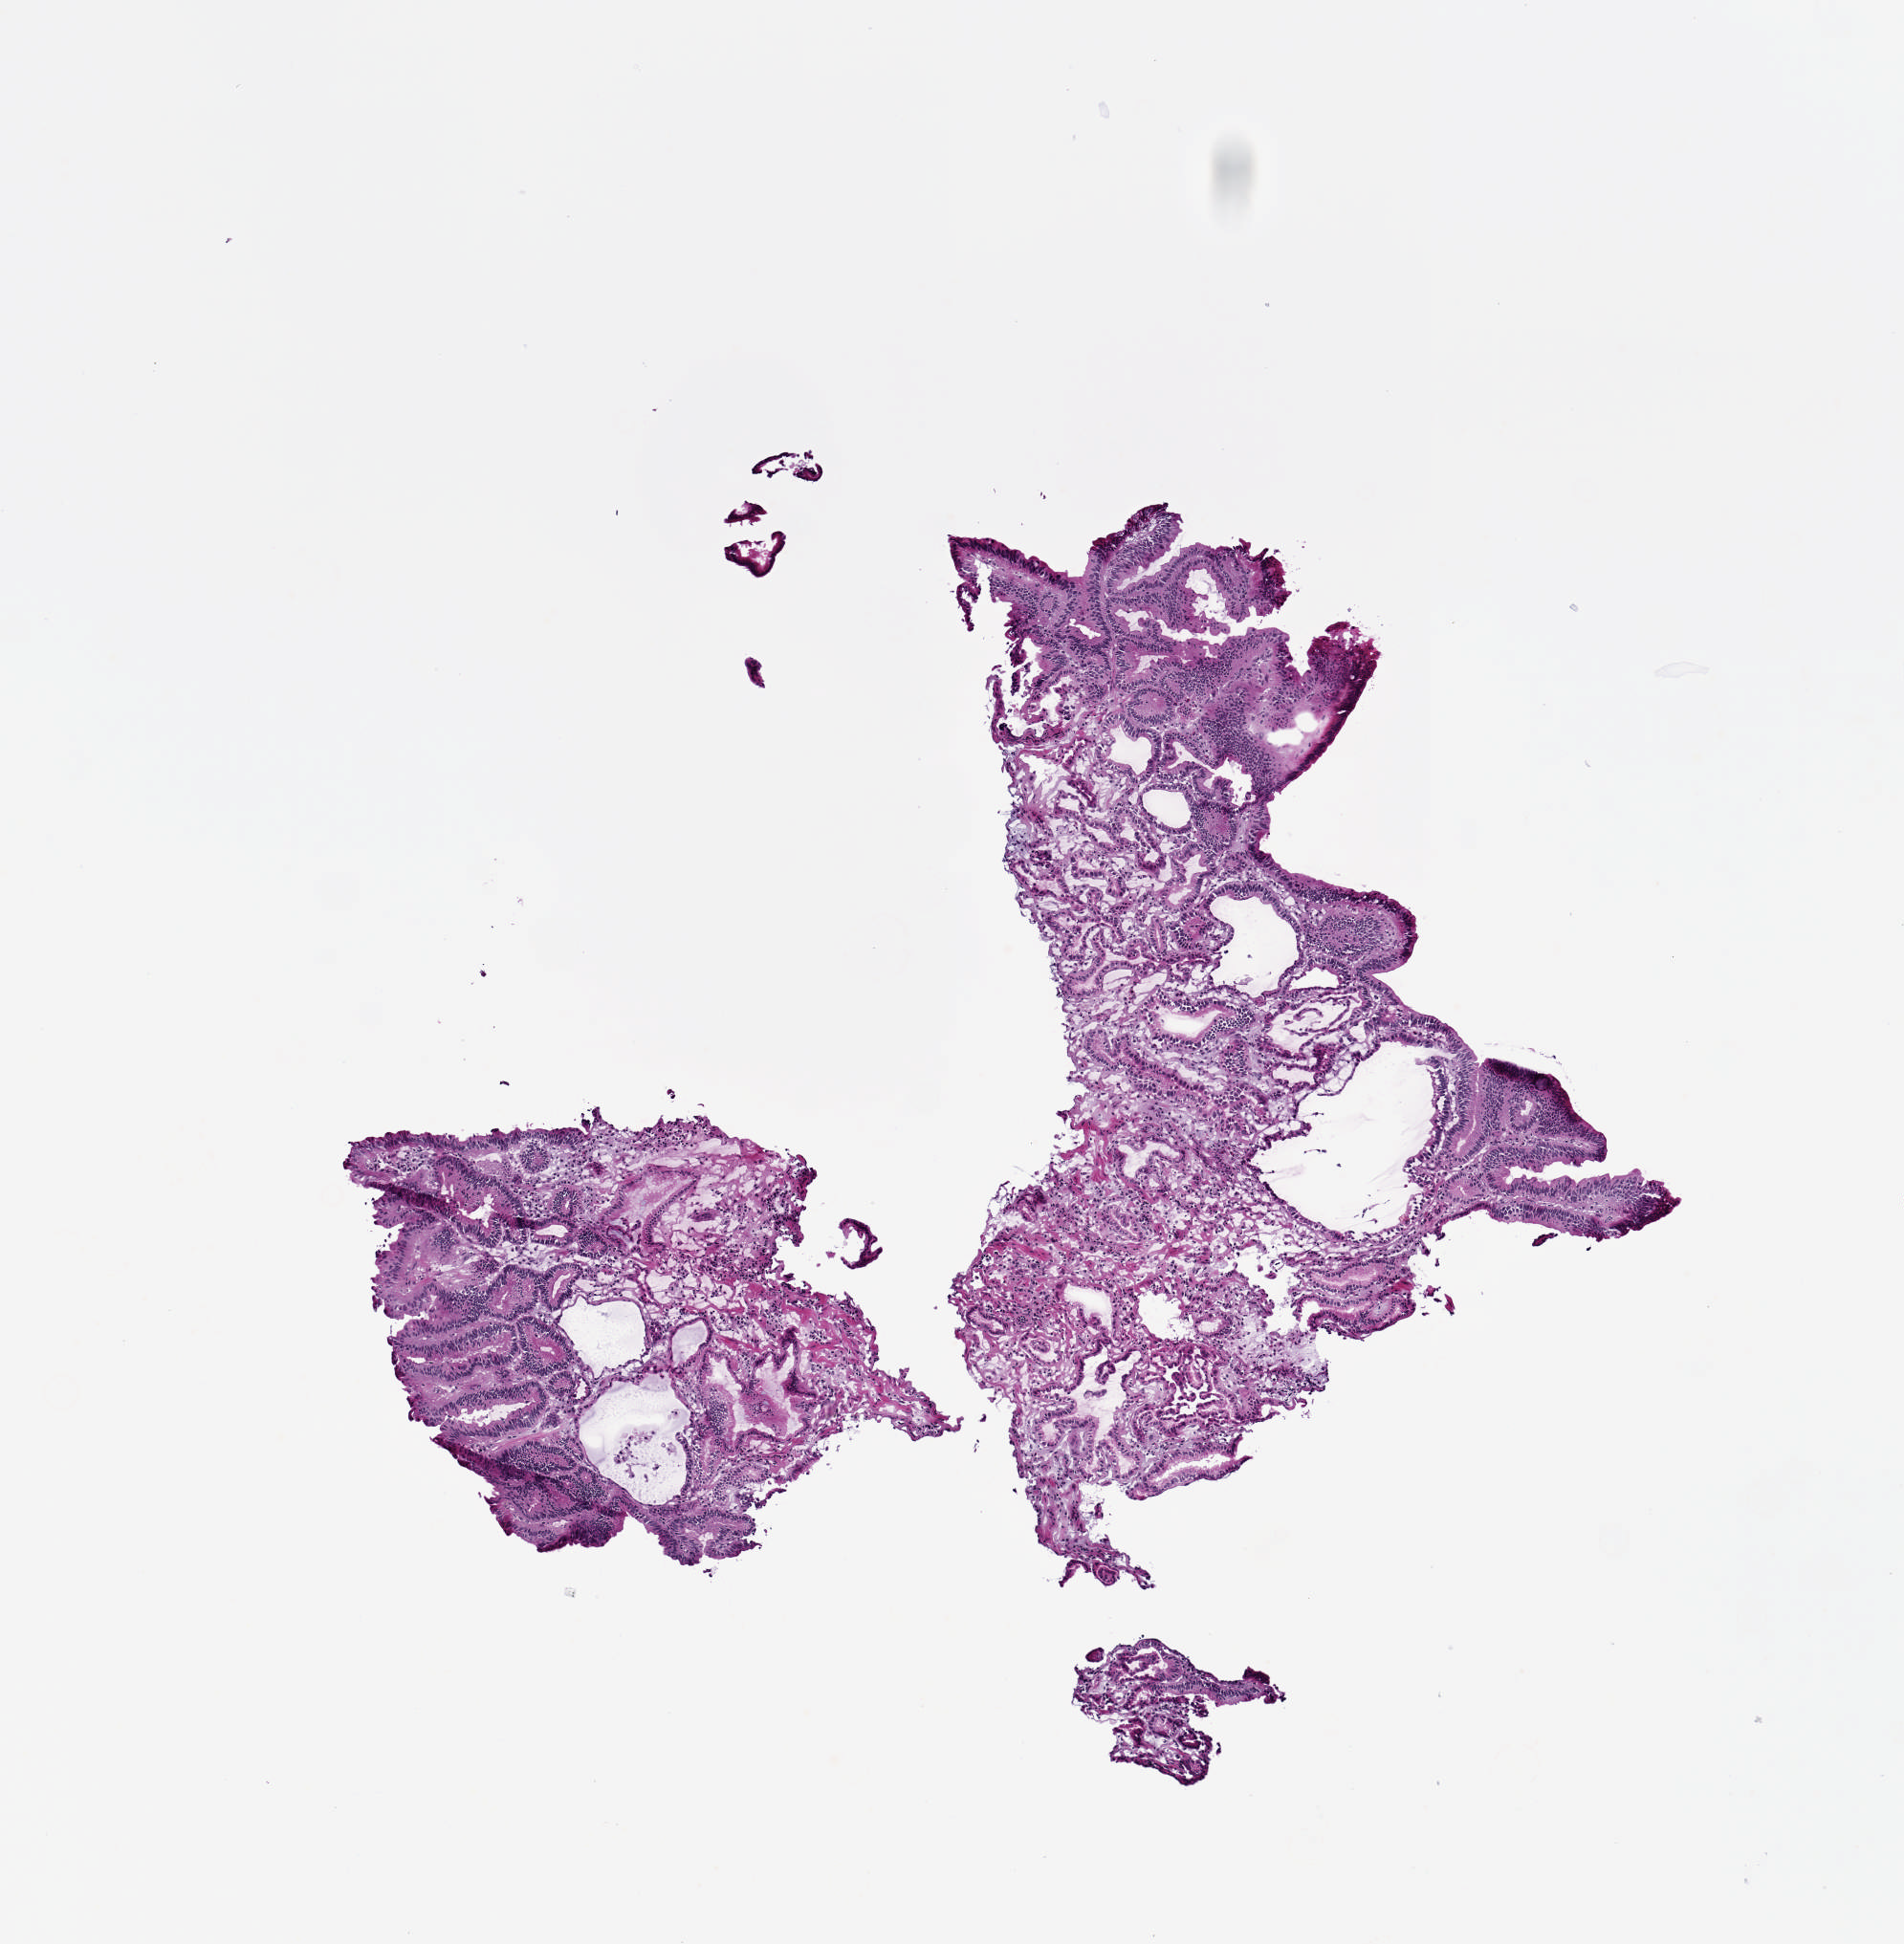
Whole-slide histology image, H&E — a low-resolution overview of the entire scanned area, about 4.0 x 4.1 mm (from a 20x scan), frozen section from the top of the tissue portion, esophagus, solid tissue normal (non-tumour tissue) sample. Male, age 74 years at initial diagnosis. Pathologist review of this section (percent, as recorded): tumour cells 0%, tumour nuclei 0%, normal cells 100%, stromal cells 0%, necrosis 0%. Inflammatory infiltration, as recorded: lymphocyte infiltration 5%, monocyte infiltration 0%, neutrophil infiltration 0%.
• this section: solid tissue normal sample (biorepository sample class)
• patient diagnosis: Adenocarcinoma, NOS (lower third of esophagus)